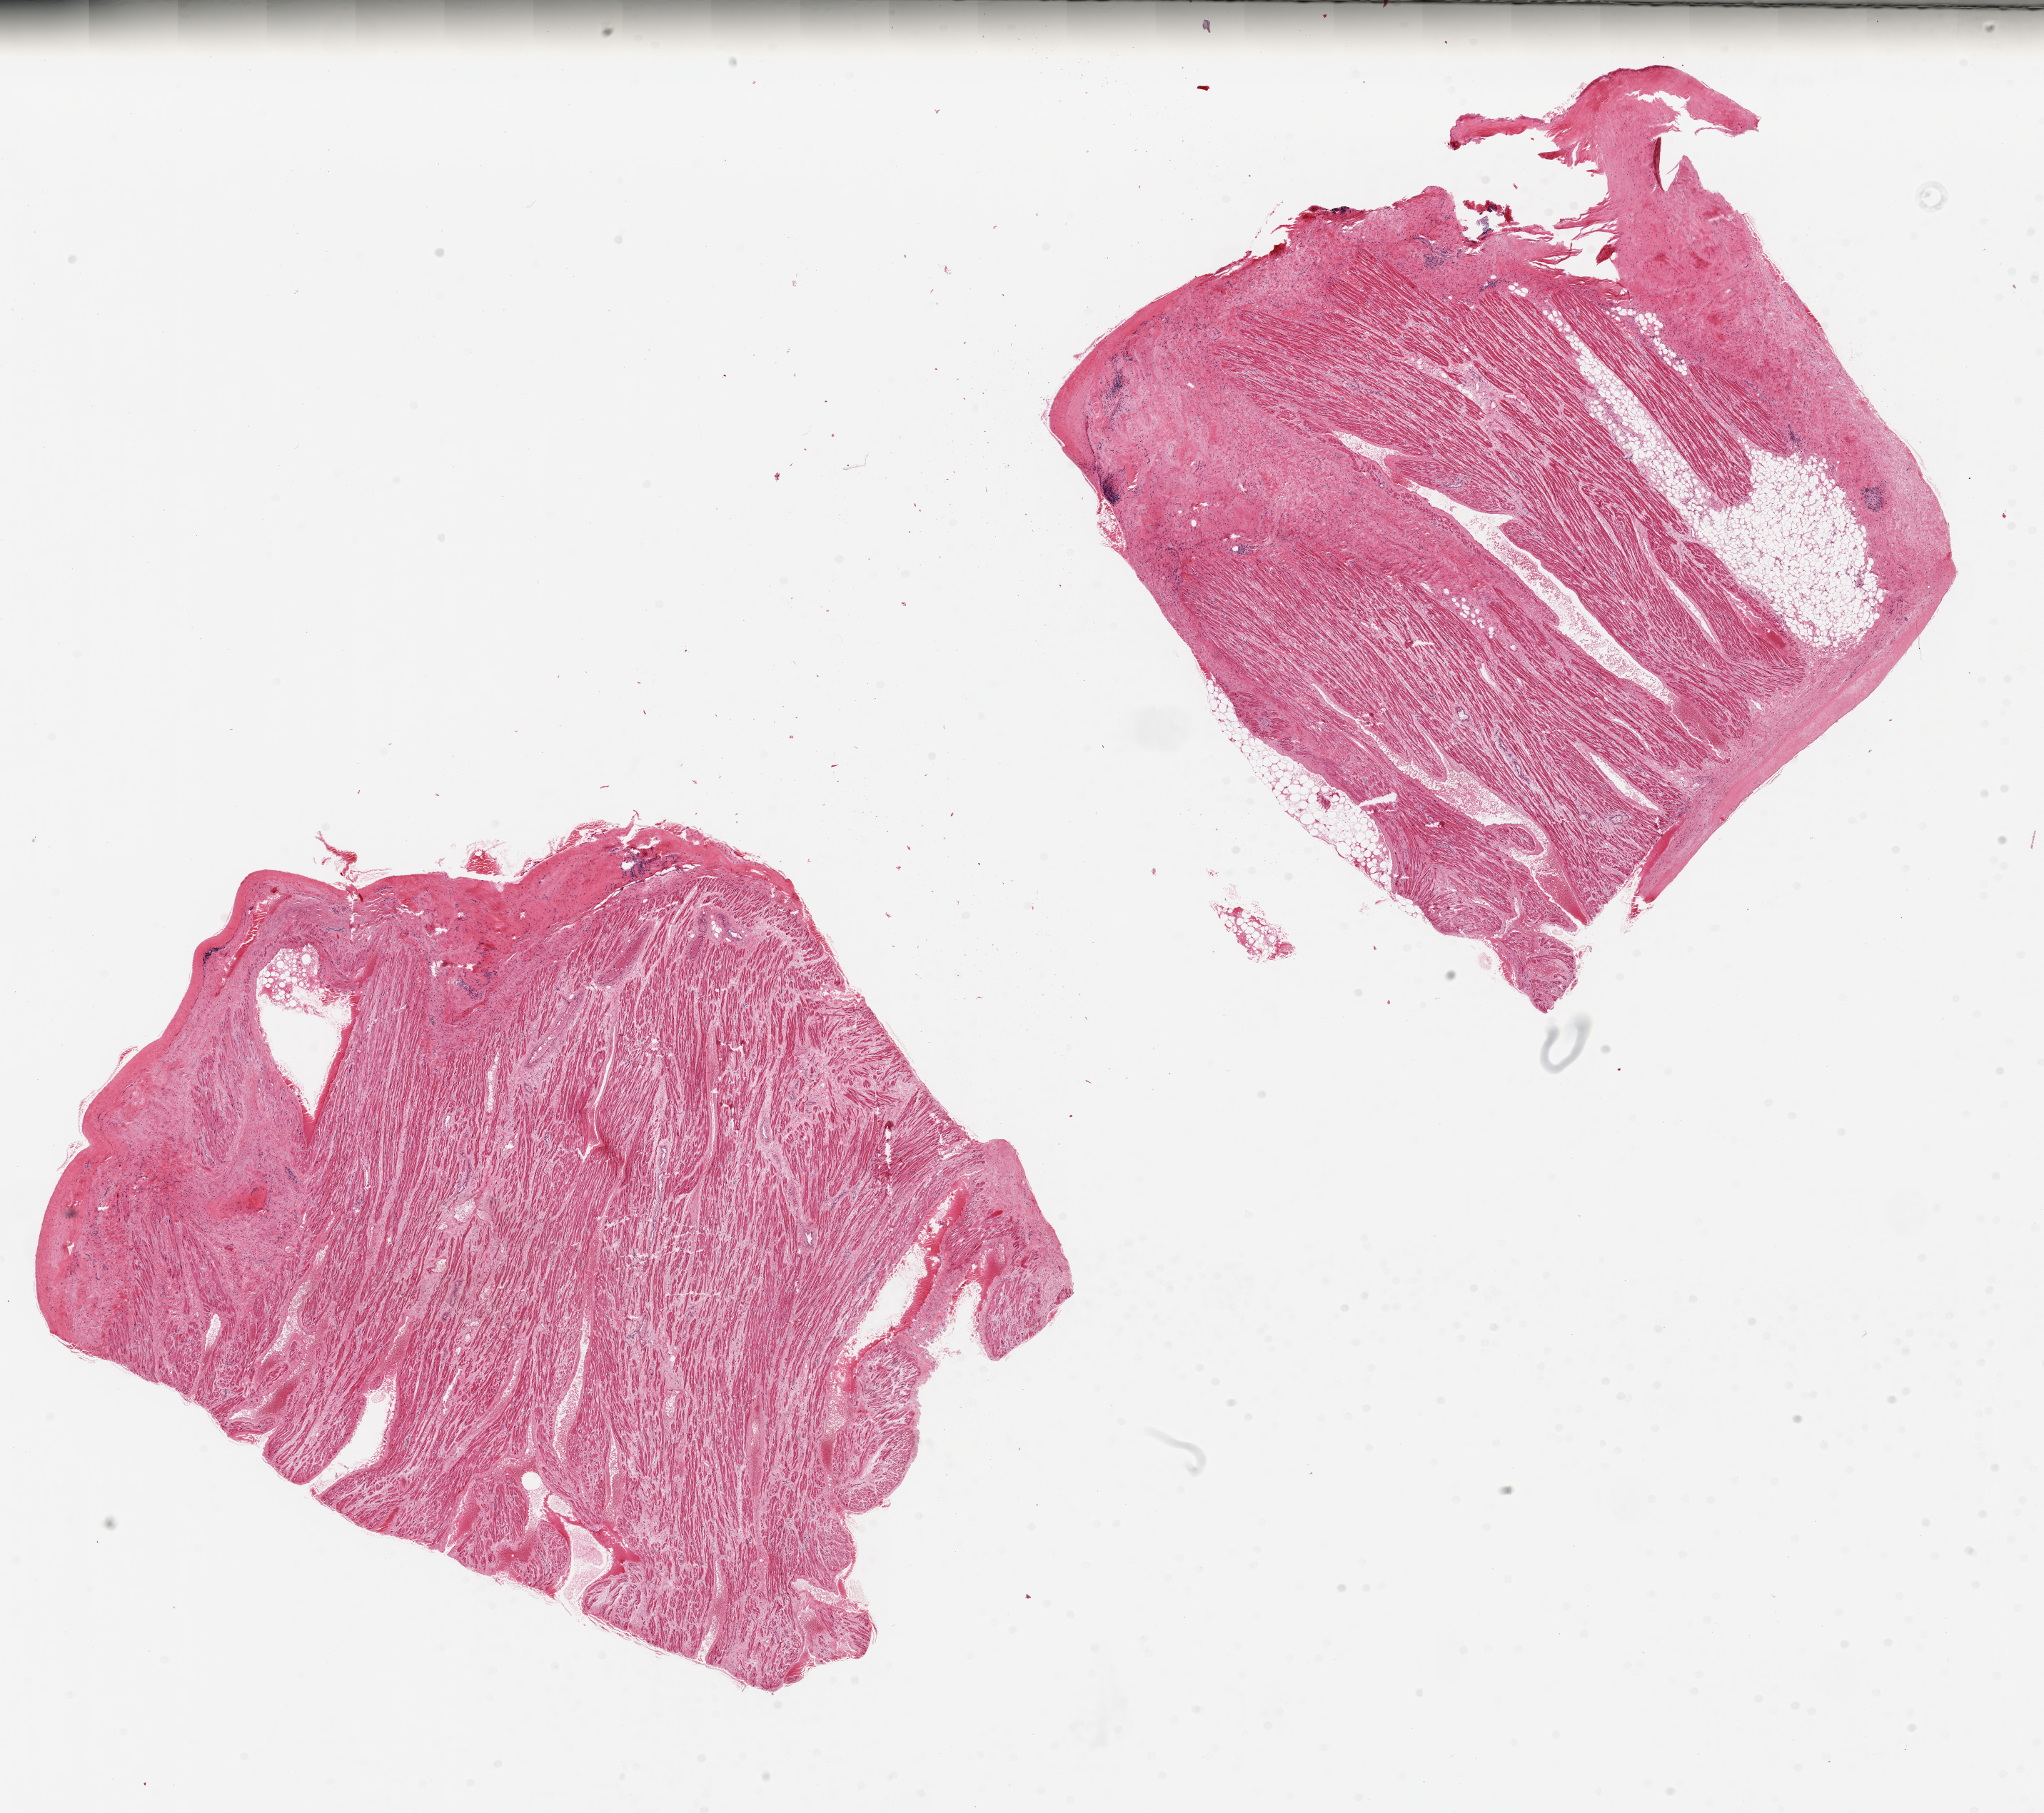
Hematoxylin and eosin (H&E) whole-slide image — a low-resolution overview of the entire scanned area, about 22.6 x 20.1 mm (from a 20x scan), PAXgene-fixed, paraffin-embedded tissue, section of auricular appendage (target tissue), donor tissue sample. Donor sex: male.
- pathologist's review note for this sample: 2 pieces